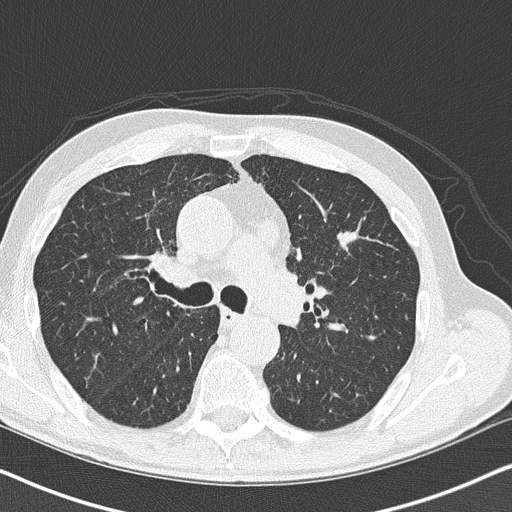
Low-dose screening chest CT, axial slice, second screening round (one year after baseline), lung window (W 1500 / L -600 HU), 2 mm slice thickness, slice 102 of 158 in the series. Male participant, aged 73 years at enrolment. Current smoker at enrolment.
• Lesion marked by an expert reader, bounding box <314,218,375,270> (left, top, right, bottom; pixels).
• The screening reader recorded 3 non-calcified nodules or masses ≥4 mm on this exam (left upper lobe, left upper lobe, right lower lobe); which of them this box marks is not recorded.
• Official screen result: positive, other.
• Lung cancer was diagnosed 36 days after this screen: small cell carcinoma, NOS, left upper lobe, stage IIIB (AJCC 6th edition), 19 mm at pathology.